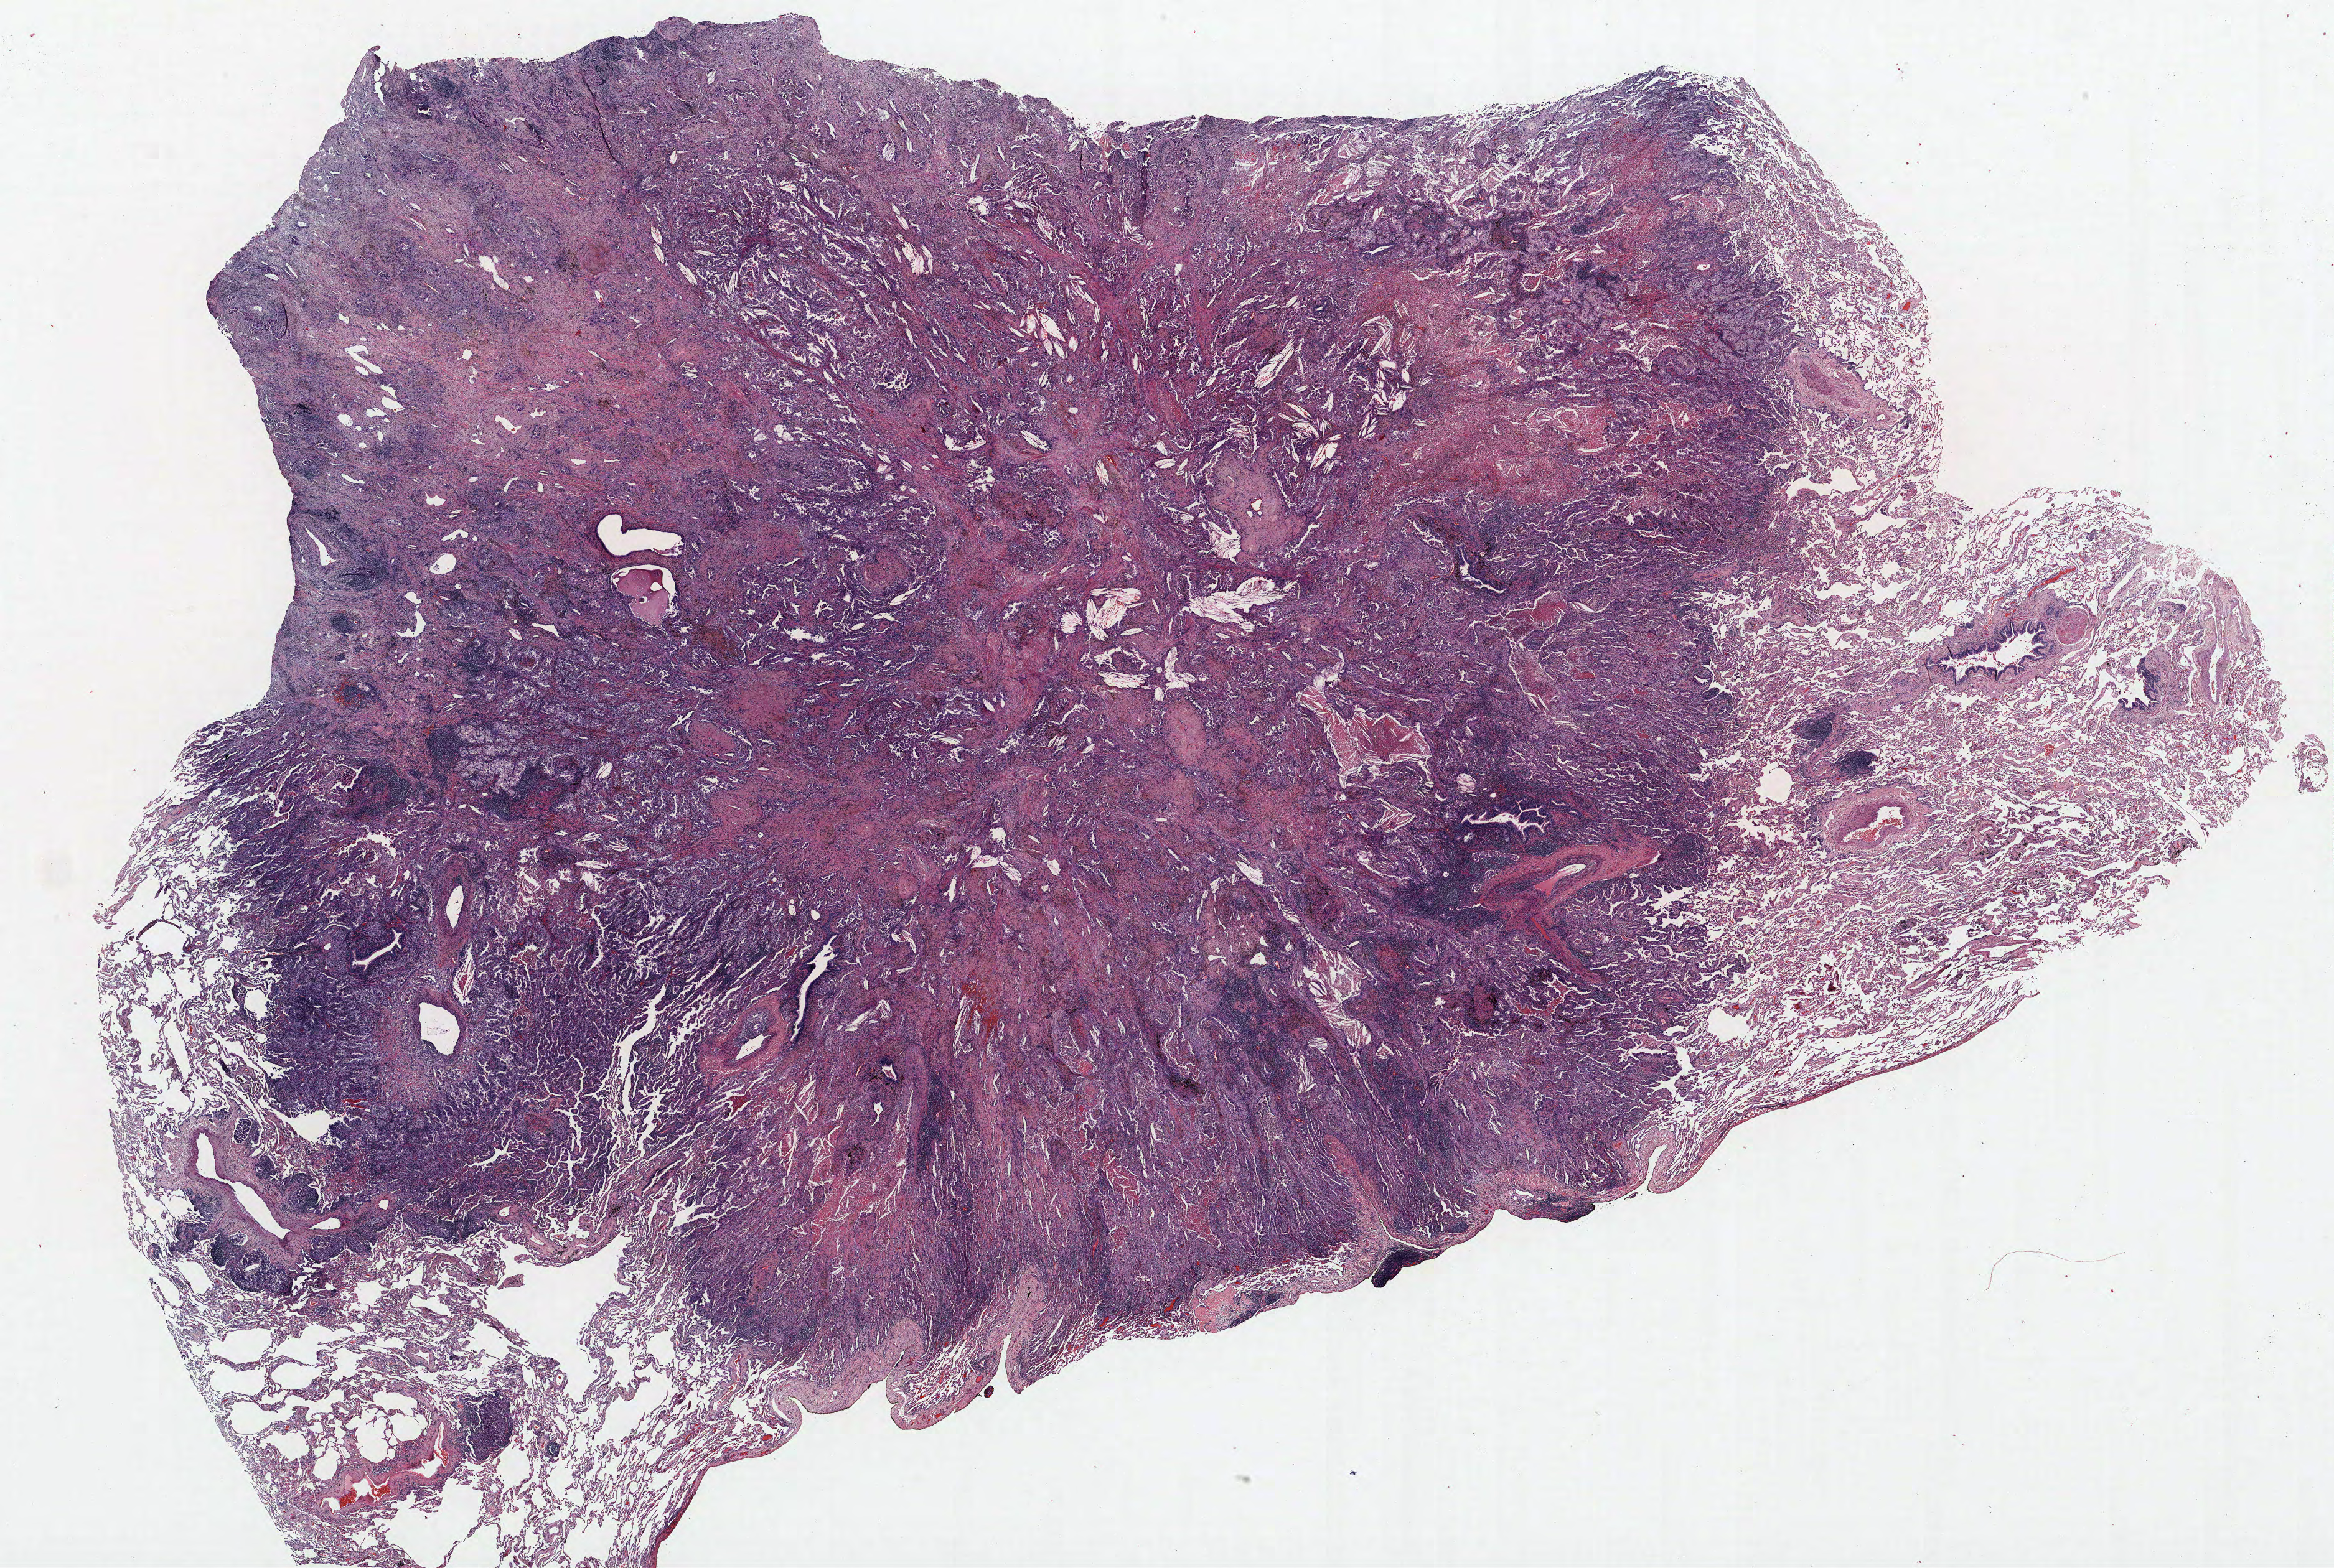
Whole-slide histology image, Hematoxylin and eosin (H&E) stained — whole scanned area (about 30.0 x 20.2 mm, slide scanned at 40x) shown as a low-resolution overview; FFPE section; lung tissue. Male patient, aged 64 at enrolment. Current smoker at enrolment. Grade: moderately differentiated (G2).
• stage (AJCC 6th edition): IA
• tumour size (pathology): 28 mm
• ICD-O-3 topography: lower lobe of lung (C34.3)
• primary tumour location (clinical record): right lower lobe
• participant's lung-cancer diagnosis: Adenocarcinoma, NOS